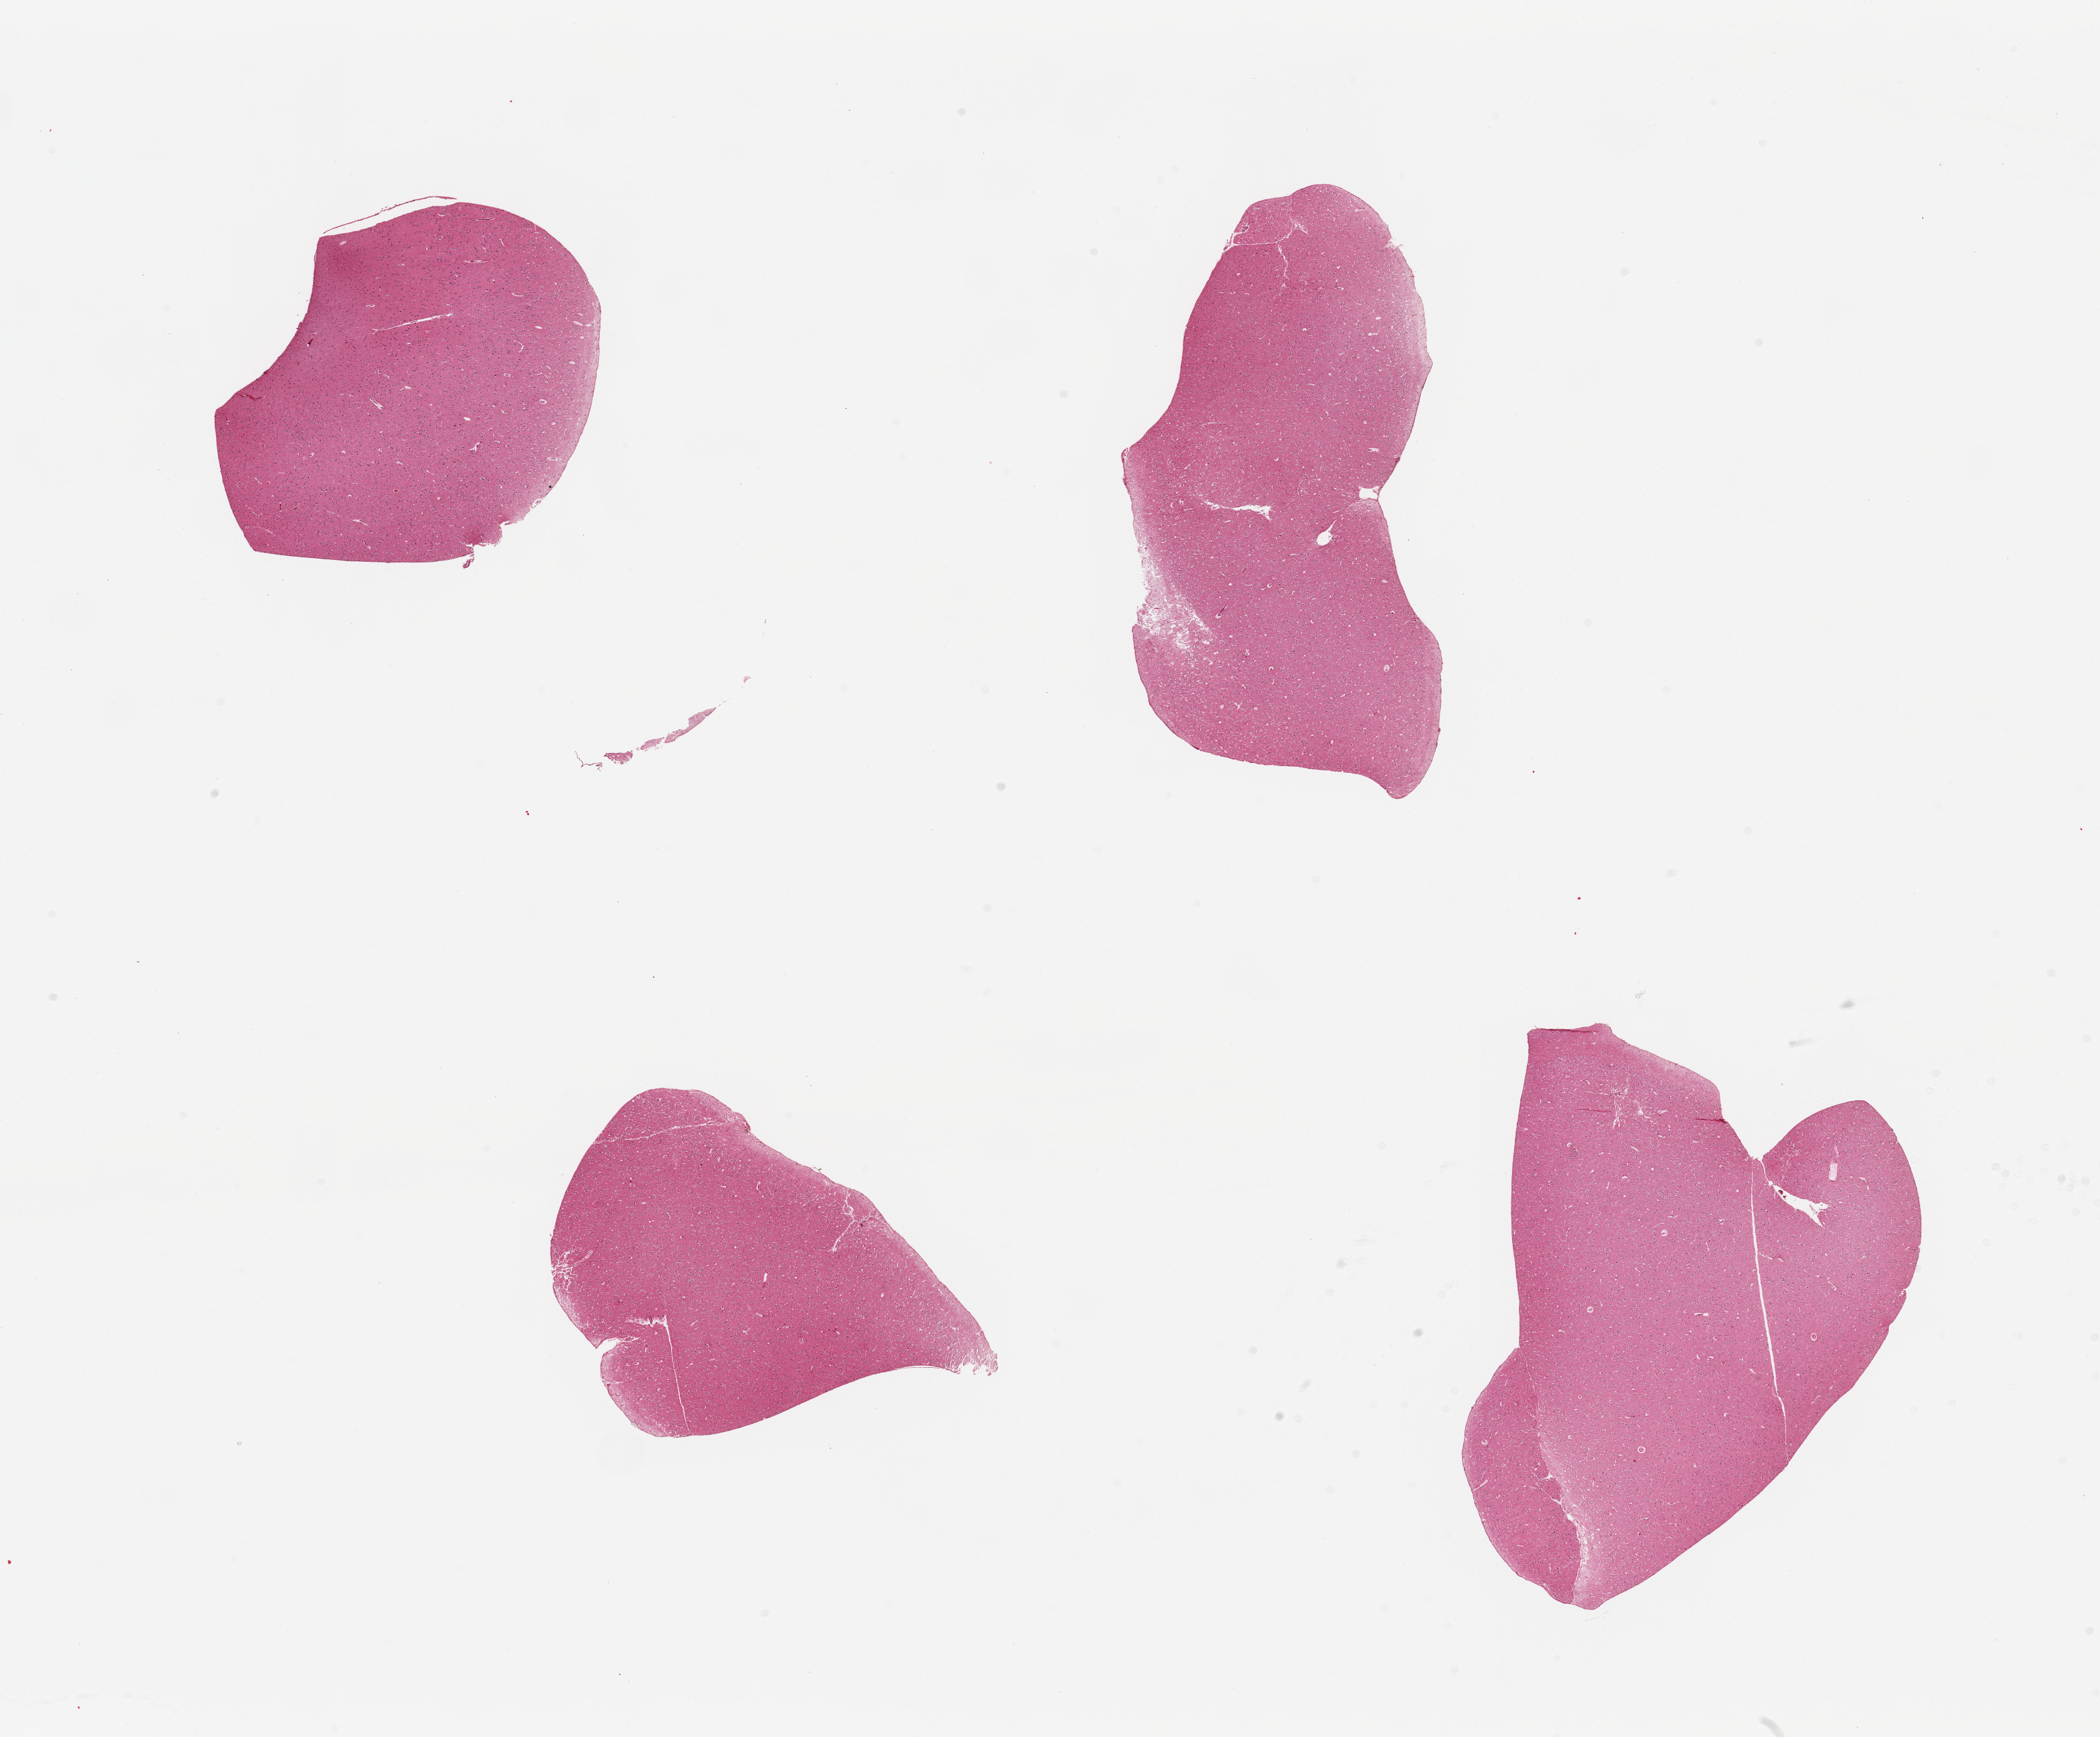
Hematoxylin and eosin (H&E) whole-slide image — whole scanned area (about 26.6 x 22.0 mm, slide scanned at 20x) shown as a low-resolution overview, PAXgene-fixed, paraffin-embedded tissue, target tissue: cerebral cortex, donor tissue sample. Donor: female.
- pathologist's review note for this sample: 4 pieces